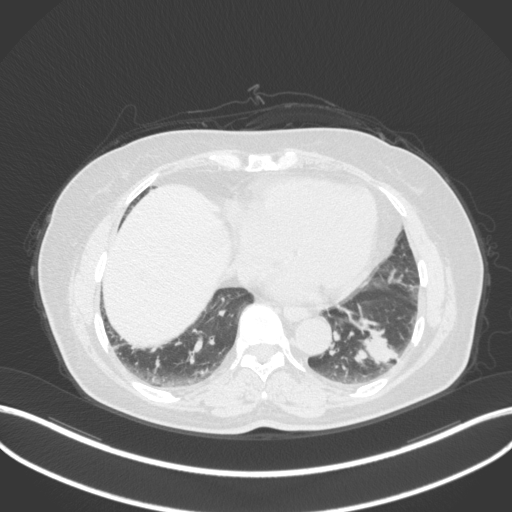
Chest CT, one axial slice. Slice 124 of 307 in the series (ordered by position). Reconstruction kernel B31f. 120 kVp. Lung window (W 1500 / L -600 HU). 1 mm slice thickness. 512 × 512 image matrix, field of view 400 × 400 mm. Female patient, age 59 years. From the clinical record (not read from this slice): clinical TNM (as recorded): T2a N0 M0.
Structures marked on this image (rectangle marked by the reading radiologist):
- lung tumour (recorded histology: adenocarcinoma): bounding box [x1, y1, x2, y2] px = [348, 323, 398, 371]